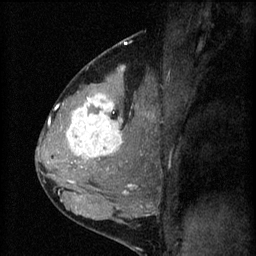
Breast MRI (dynamic contrast-enhanced), one sagittal slice. Slice 37 of 60 in the series (ordered by position). 3 images stored at this slice position (order not interpretable as contrast timing). 1.5 T. TE 4.2 ms, TR 8.2 ms. 256 × 256 image matrix. Female patient, age 37 years.
Outlined on this slice (semi-automatic segmentation, software-assisted and operator-edited):
- analysis volume of interest (the breast-tissue region the enhancement analysis was run in; not a lesion): box from (x=53, y=78) to (x=140, y=181) px
- tumour enhancement mask (voxels above the 70 % enhancement threshold inside the analysis volume of interest): (x=62, y=96)–(x=122, y=181)